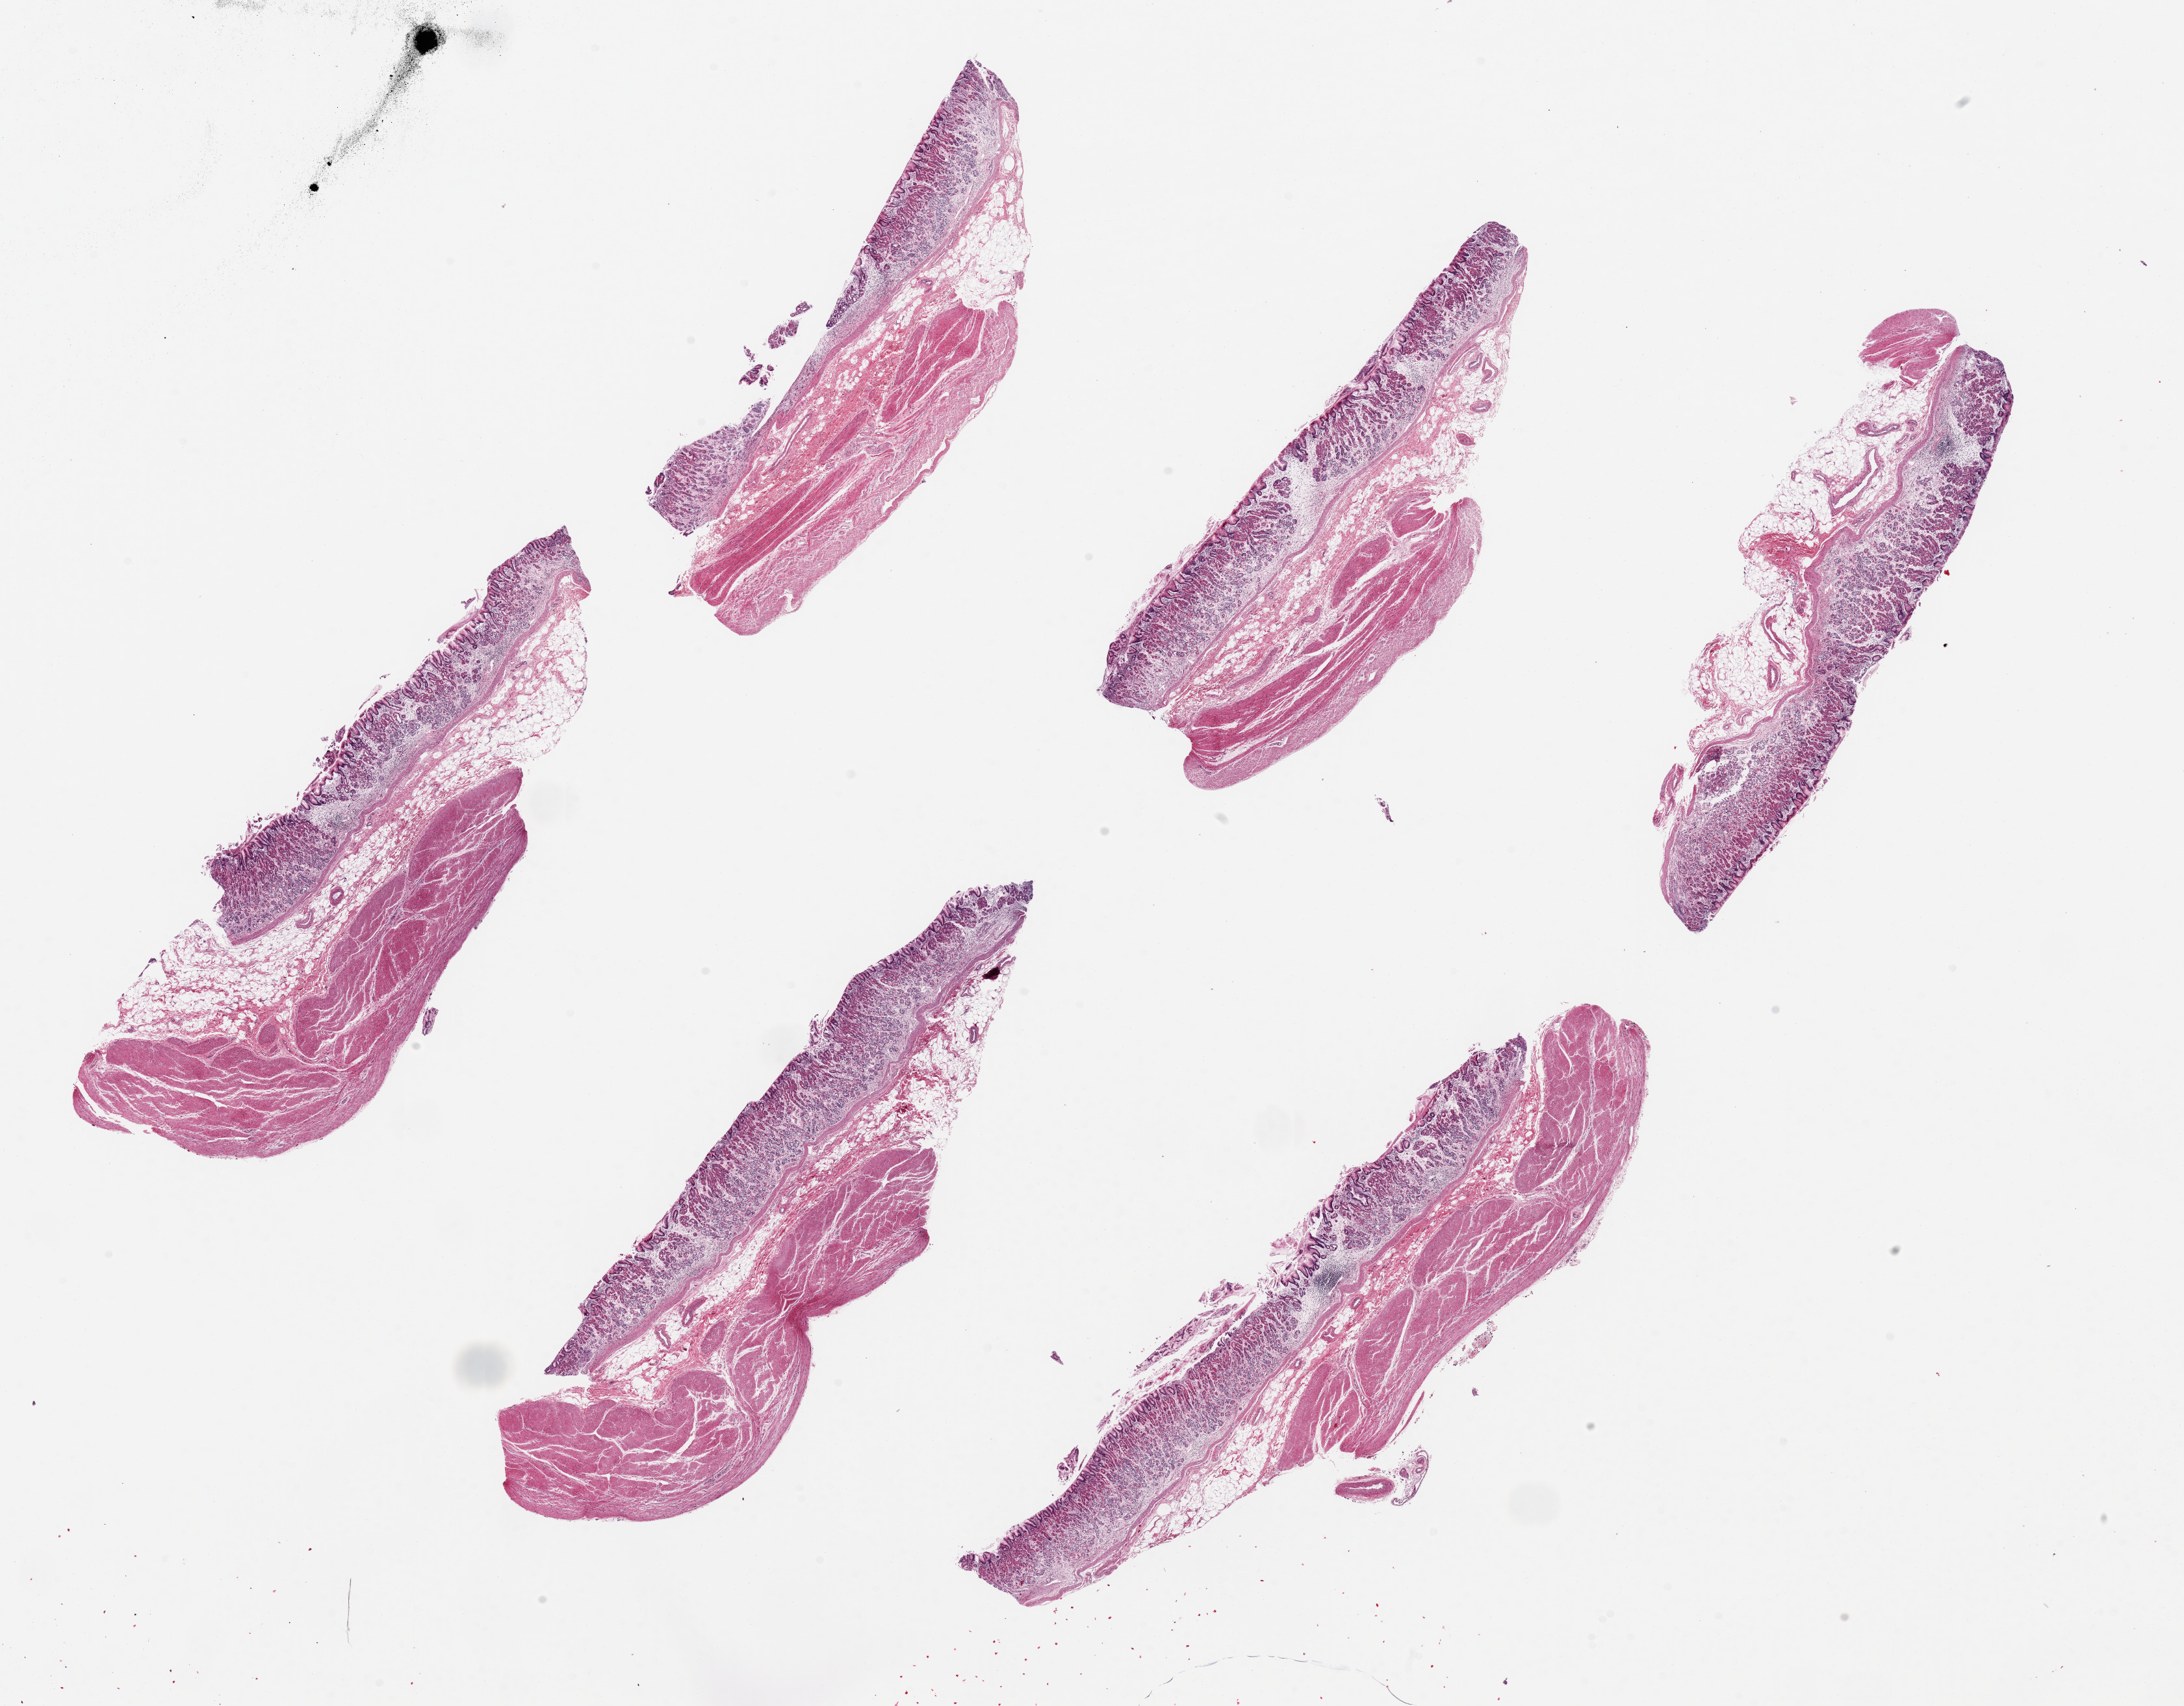
Whole-slide image, haematoxylin and eosin stain — whole scanned area (about 26.6 x 20.8 mm, from a 20x scan) shown as a low-resolution overview; PAXgene-fixed, paraffin-embedded tissue; target tissue: stomach; tissue donor sample. Donor sex: male.
Reviewer comment on this tissue sample: 6 pieces, up to 3x9.7mm; mucosa partially autolyzed.